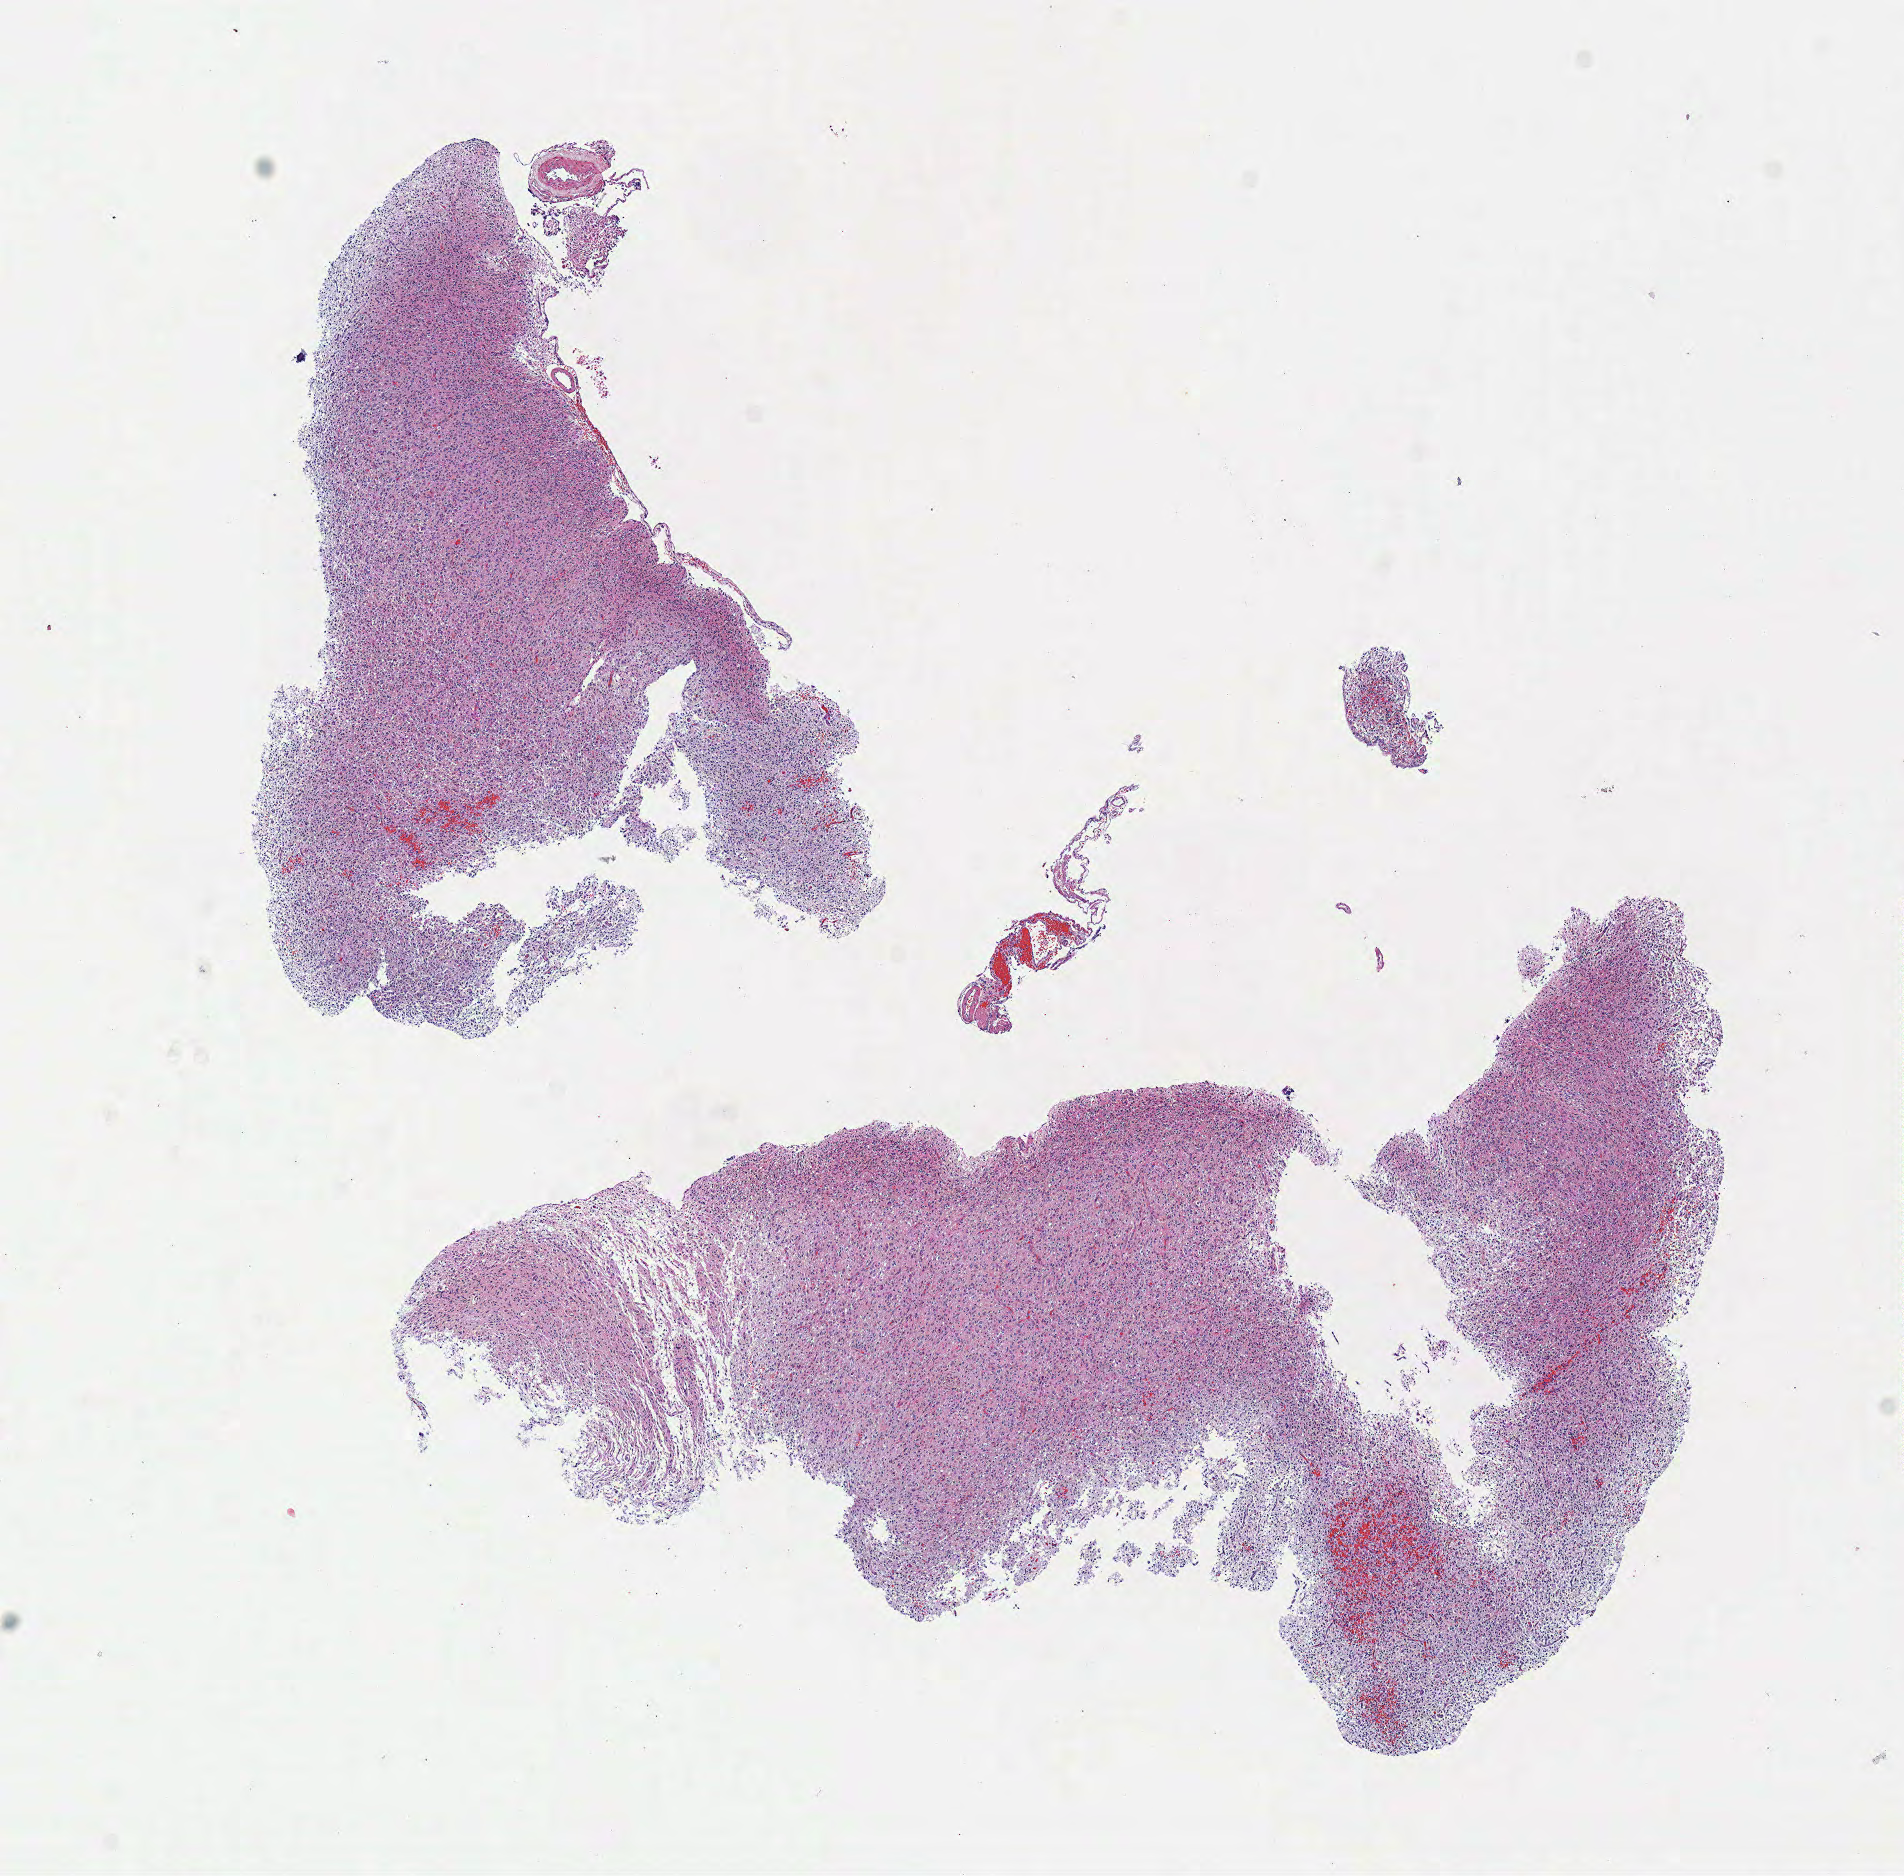
Digitized Hematoxylin and eosin (H&E) stained tissue section (whole slide) — whole scanned area (about 7.5 x 7.4 mm, slide scanned at 40x) shown as a low-resolution overview; frozen section from the top of the tissue portion; brain, primary tumour sample. Female patient; age at initial diagnosis 61 years. Histologic grade: G3 (poorly differentiated). Composition of this section per pathologist review: tumour cells 100%, tumour nuclei 80%, normal cells 0%, stromal cells 0%, necrosis 0%.
• laterality: left
• pathologic diagnosis: Mixed glioma